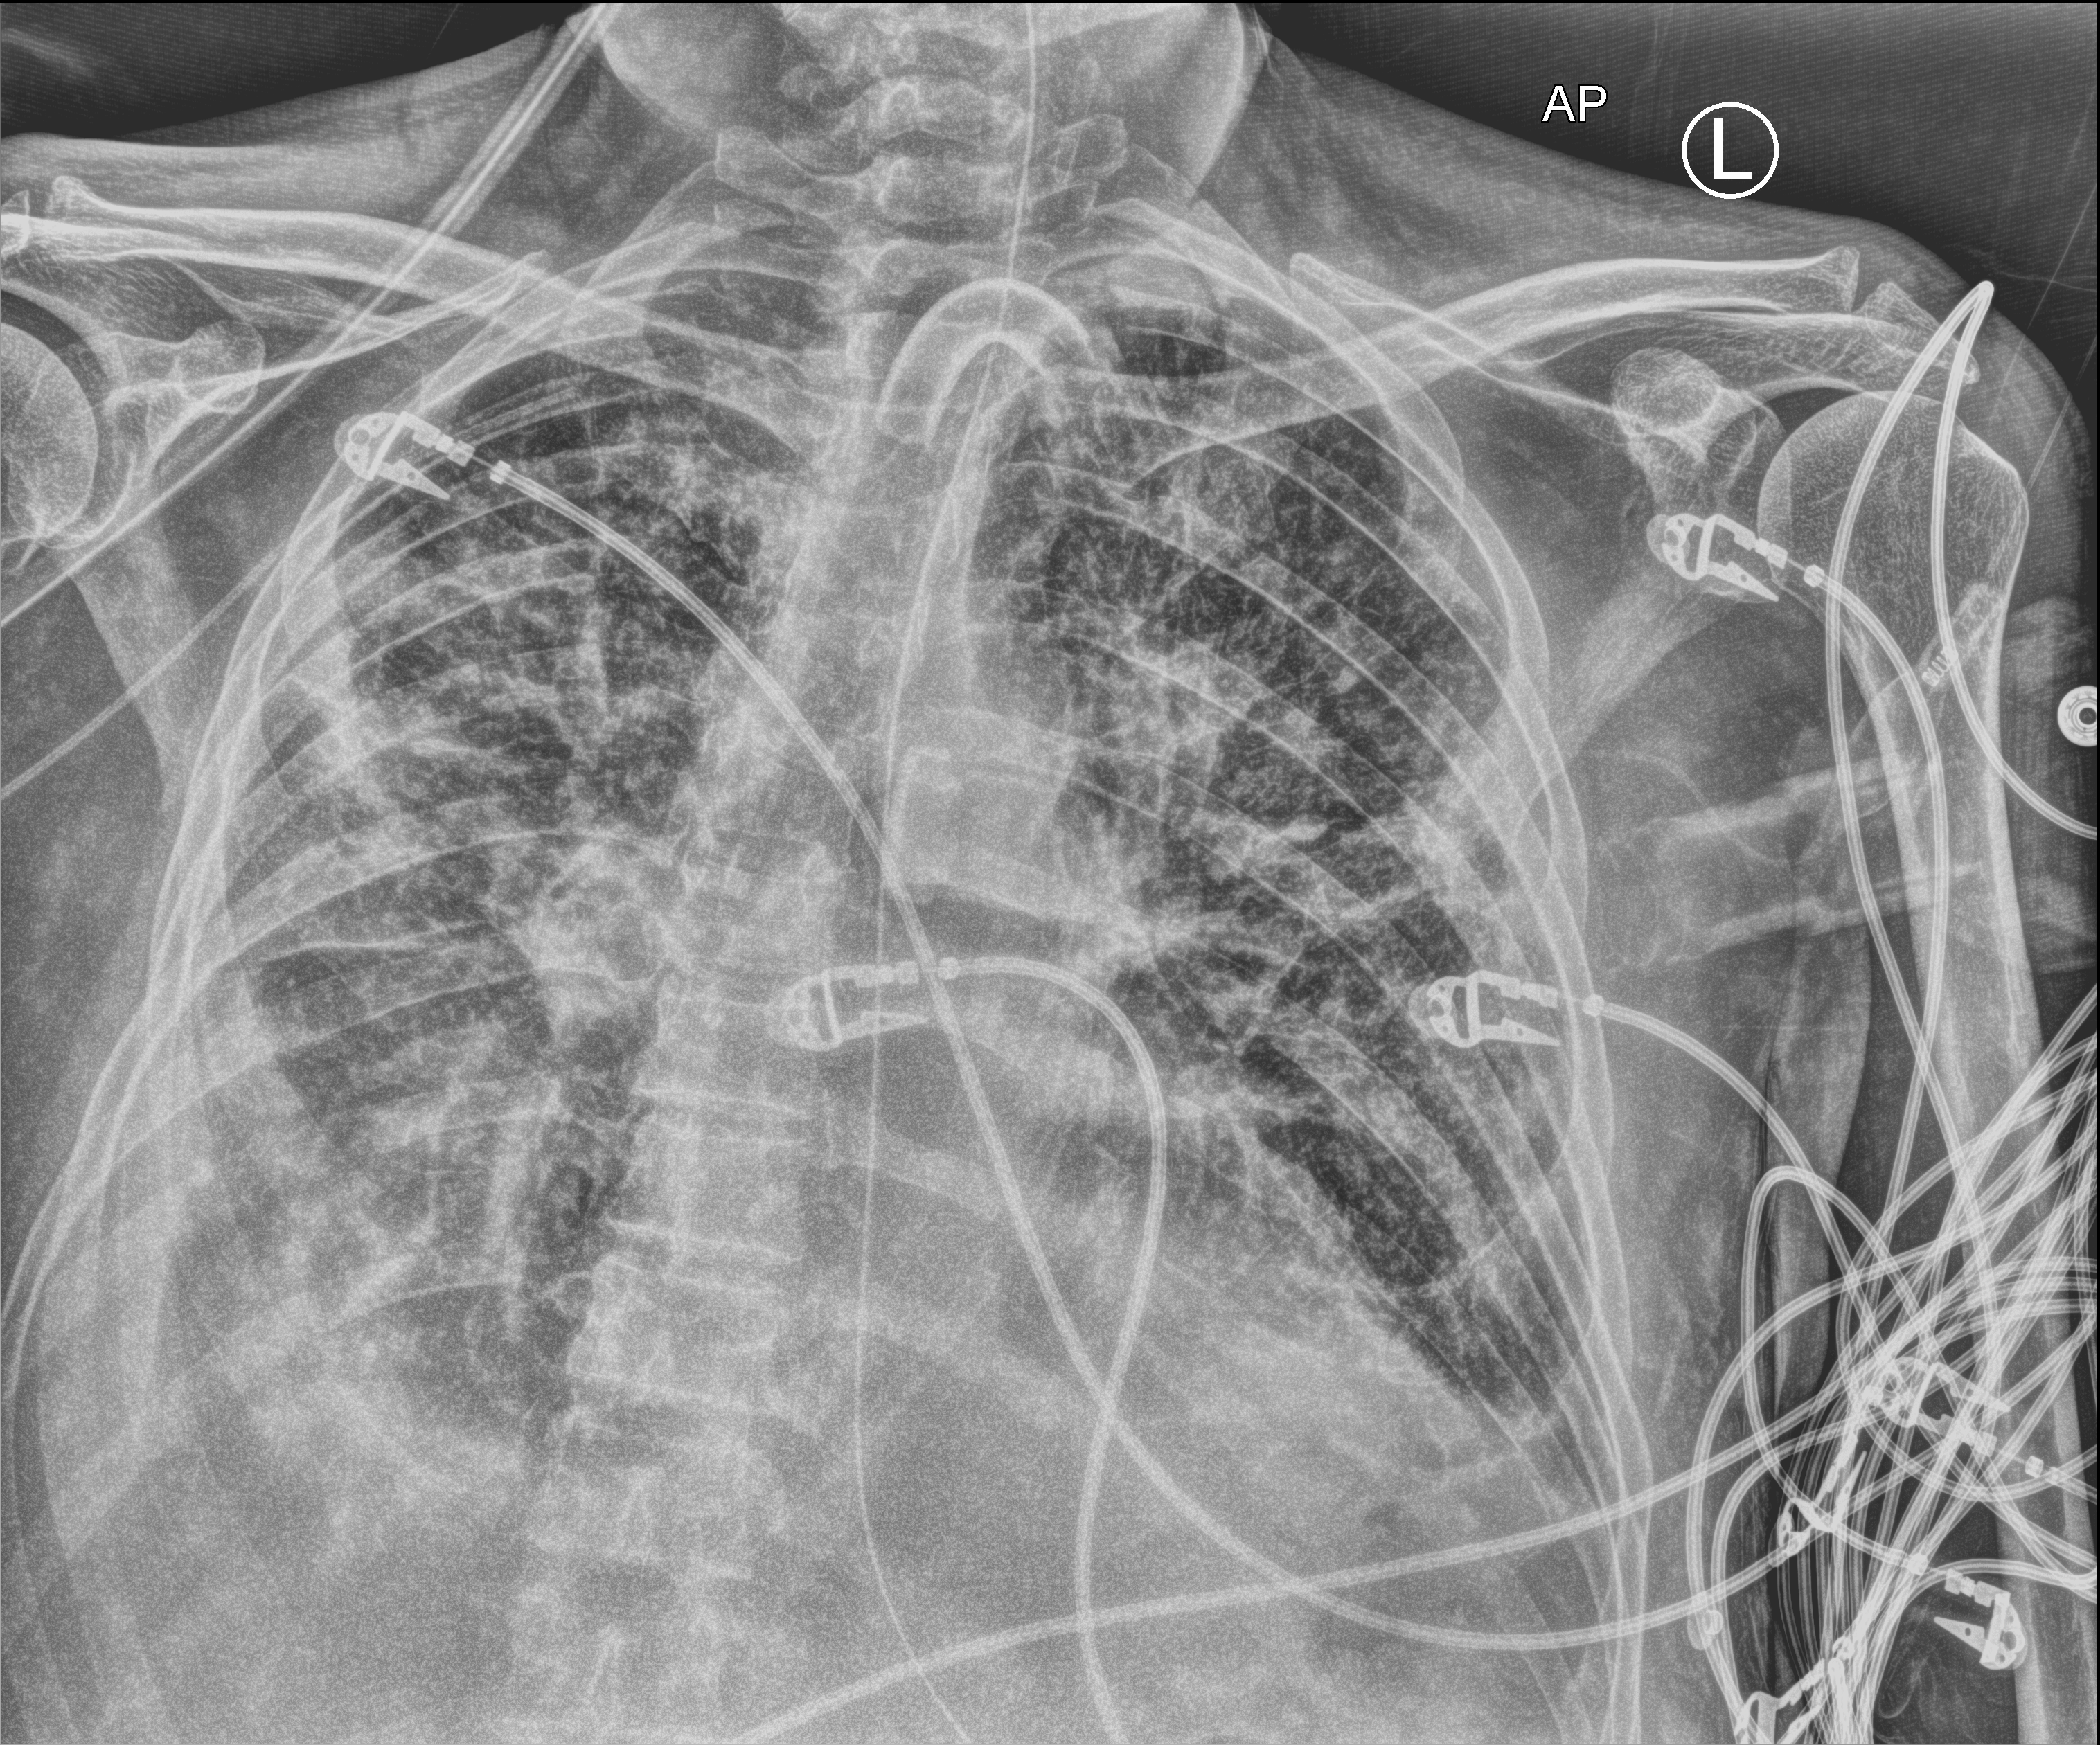
Bedside chest radiograph (computed radiography); anteroposterior (AP) projection. Male patient hospitalised with COVID-19, age 75–90 years.
Admission-level facts for this patient (not findings on this image; timing relative to this image not recorded): length of hospital stay: 70 days.